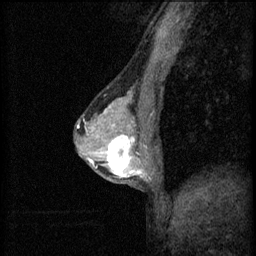
Breast MRI (dynamic contrast-enhanced), one sagittal slice; position 32 of 60 along the scan axis; 3 images stored at this slice position (order not interpretable as contrast timing); 1.5 T; TE 4.2 ms, TR 8.2 ms; 256 × 256 image matrix, field of view 180 × 180 mm. Female patient, age 44 years.
Outlined on this slice (semi-automatic segmentation, software-assisted and operator-edited):
- analysis volume of interest (the breast-tissue region the enhancement analysis was run in; not a lesion): bounding box (x1, y1, x2, y2) in pixels: (102, 132, 151, 181)
- tumour enhancement mask (voxels above the 70 % enhancement threshold inside the analysis volume of interest): (104, 134, 147, 177)